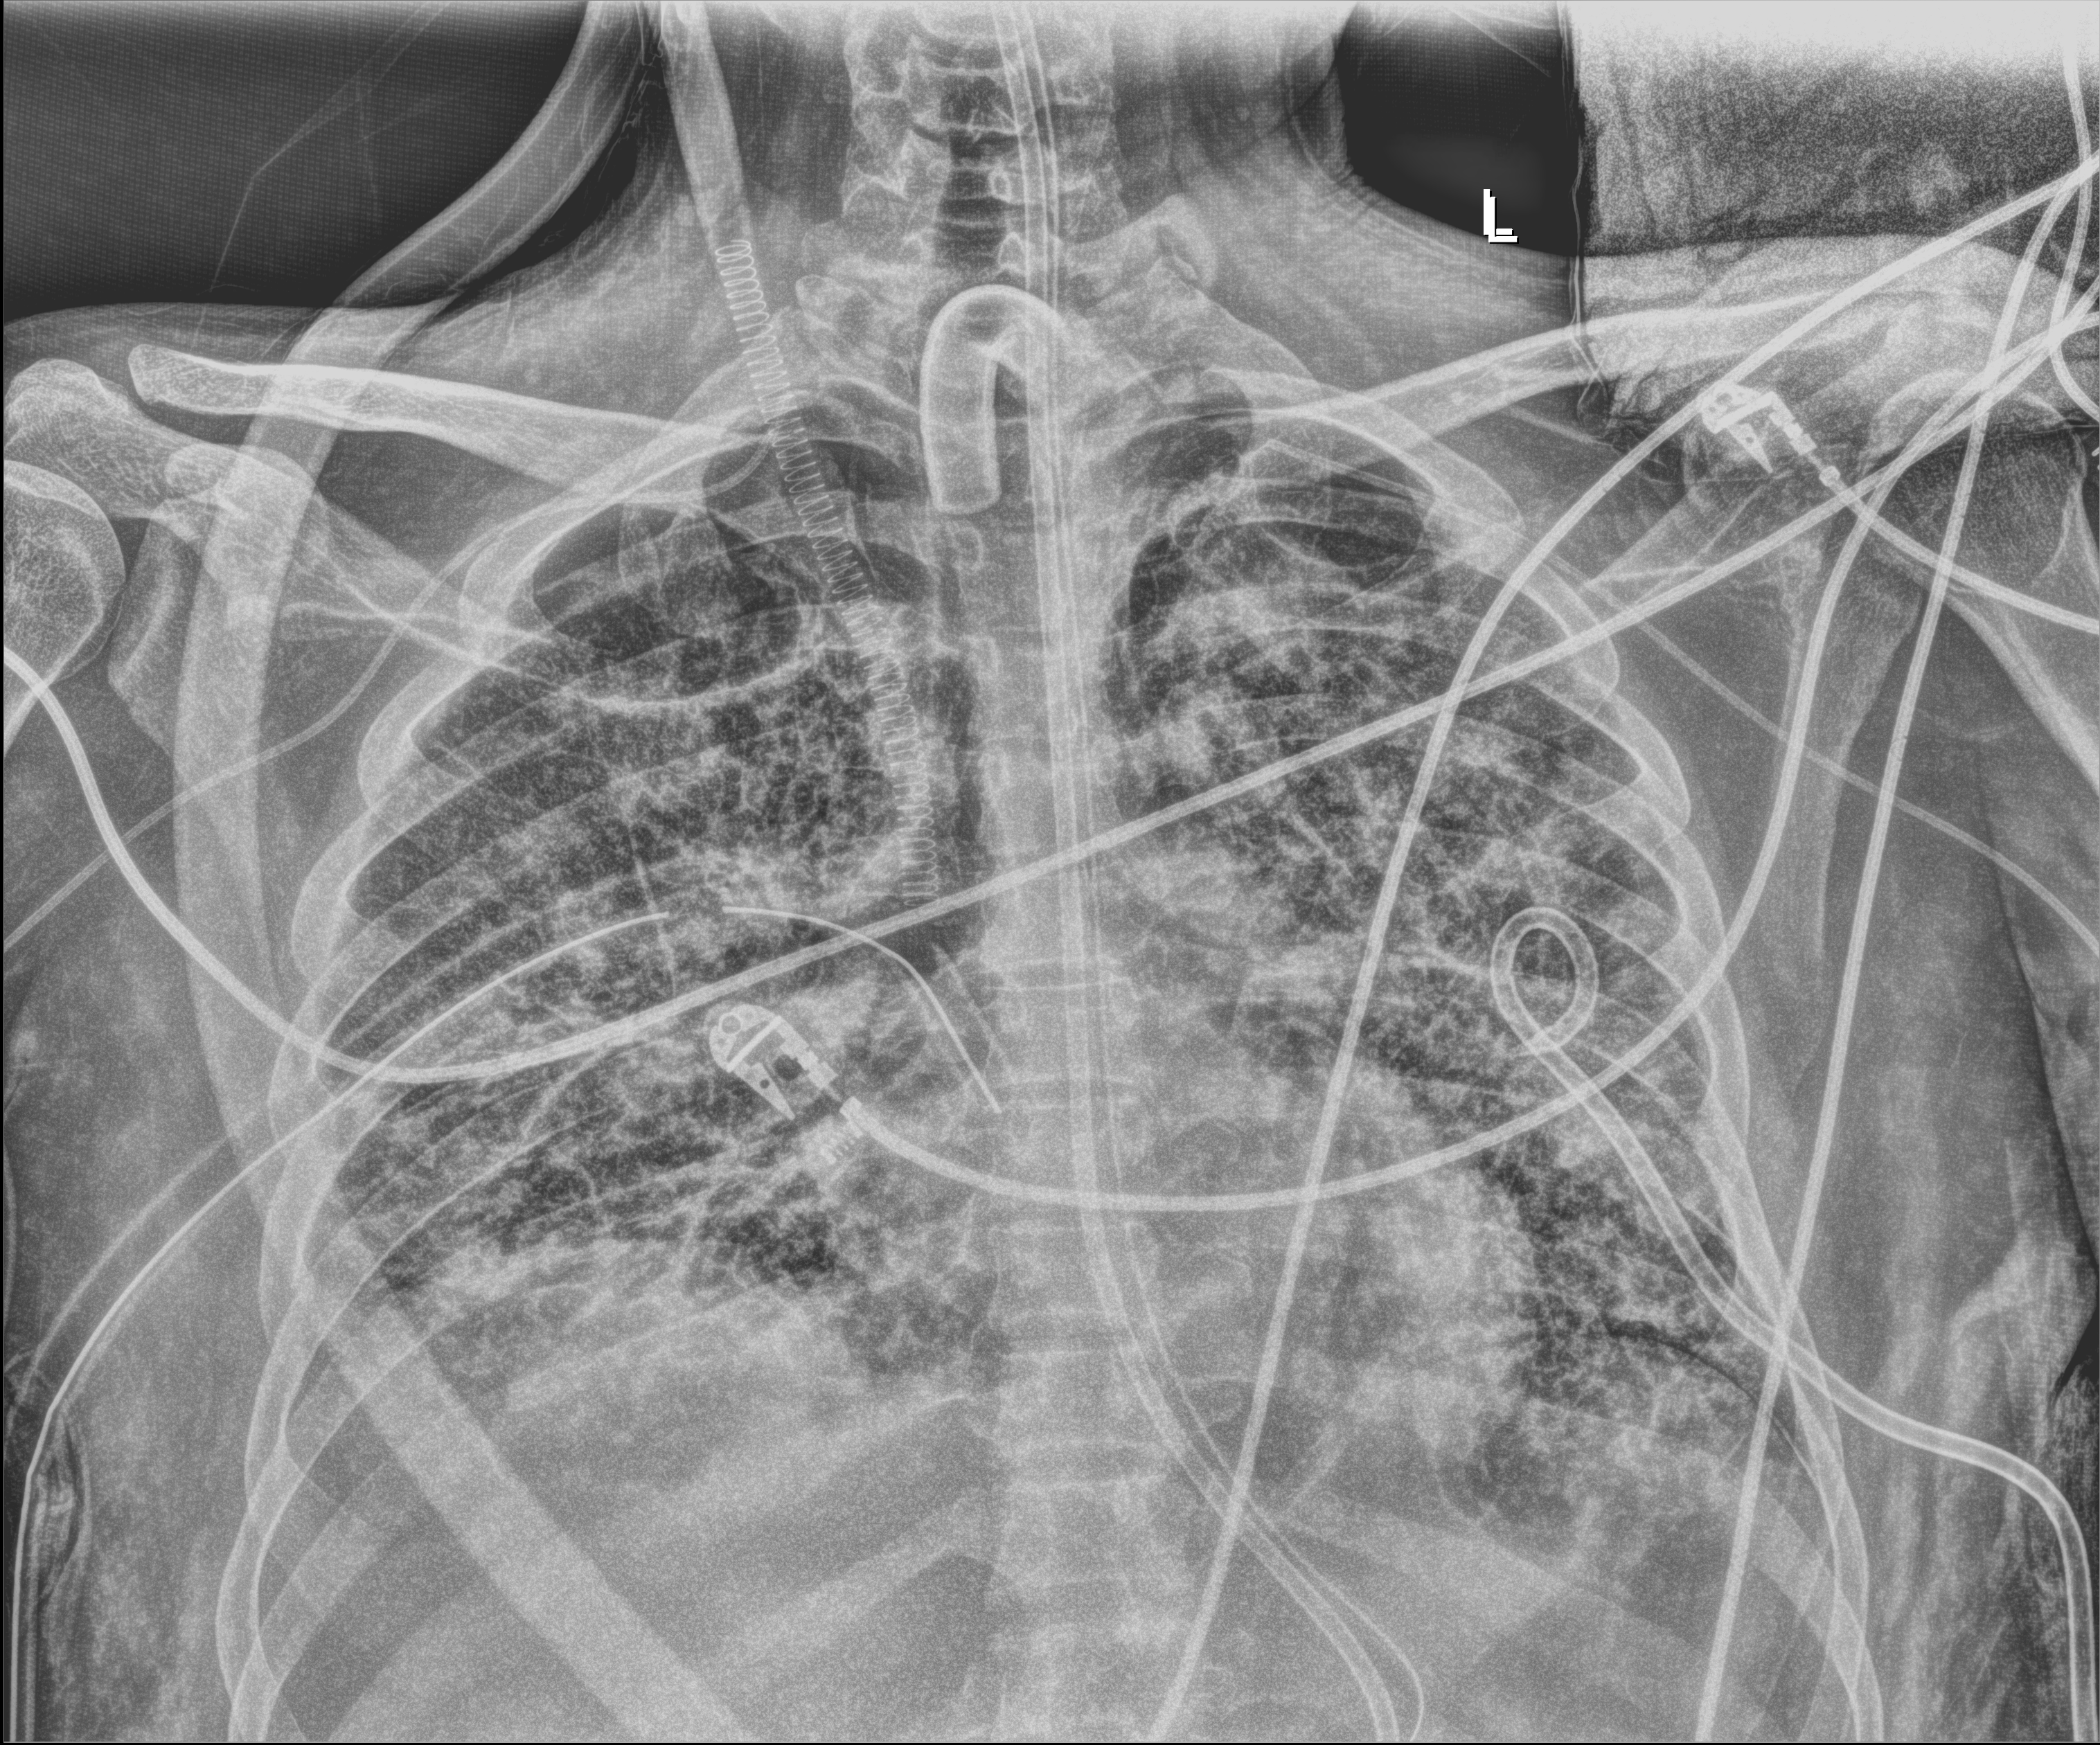
Chest X-ray, anteroposterior (AP) projection. Adult patient hospitalised with COVID-19, age 18–59 years.
From the hospital-stay record, not from the radiograph (when in the stay this image was taken is not recorded):
- smoking status (admission record): never